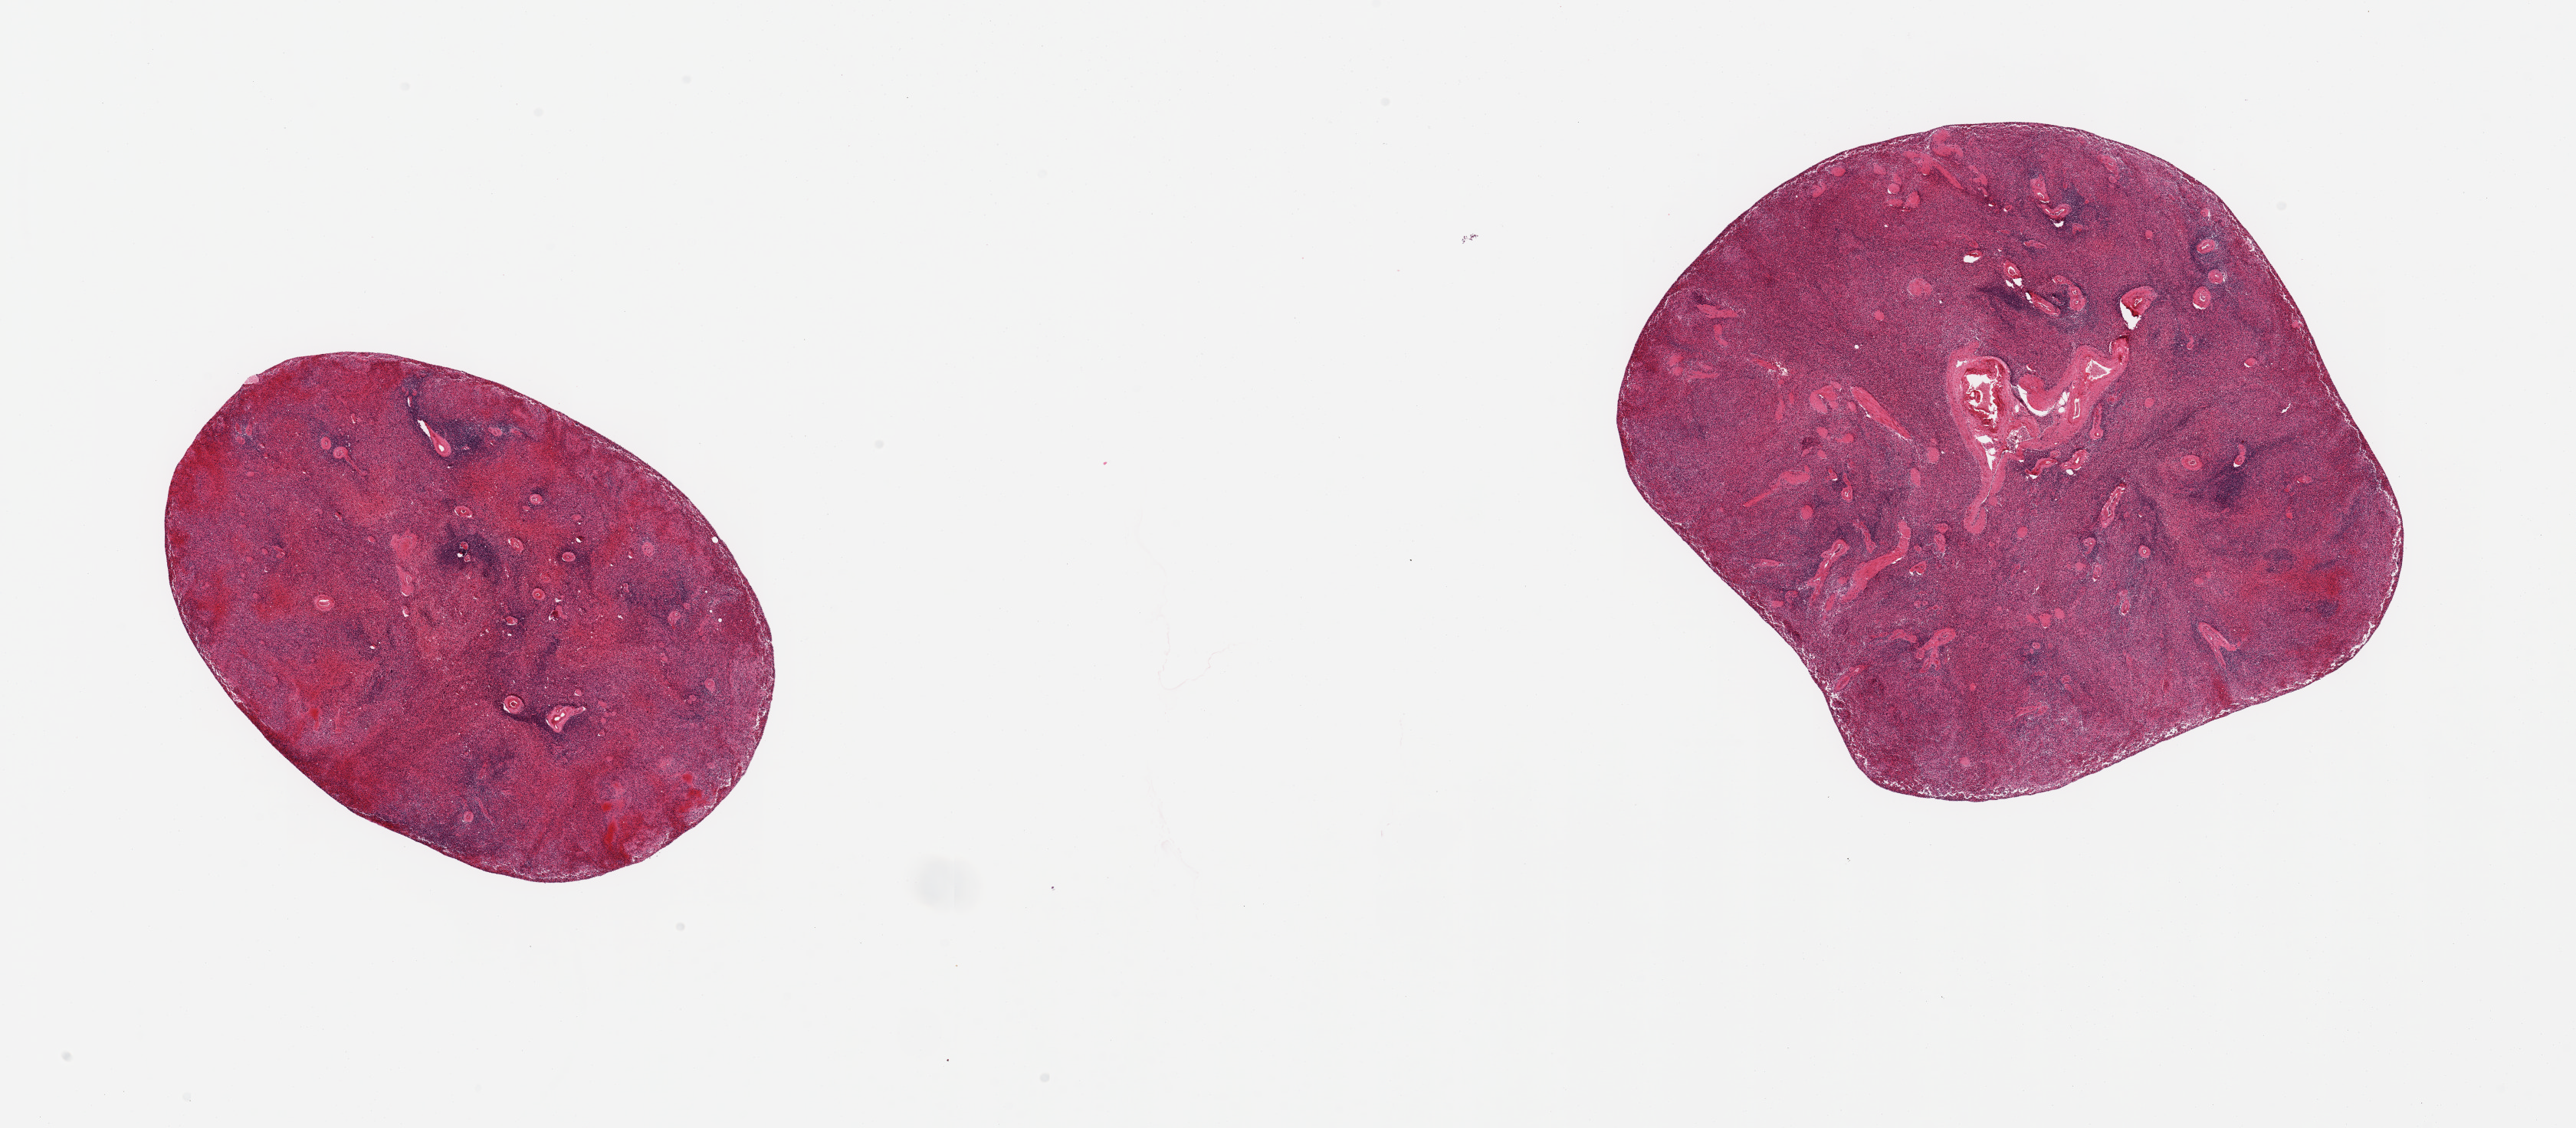
Whole-slide image, H&E stain — low-resolution overview of the scanned area, about 26.6 x 11.6 mm (acquisition: 20x scan). PAXgene-fixed paraffin-embedded (PFPE) section. Target tissue: spleen. Tissue donor sample. Donor: female.
* pathologist's review note for this sample: 2 pieces; focal congestion